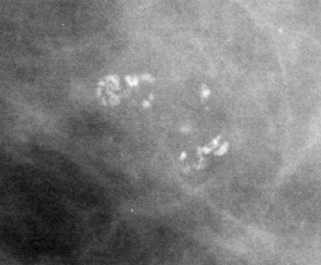
Cropped region of a digitized screen-film mammogram centred on a radiologist-marked abnormality; left breast; CC view.
Calcifications, morphology pleomorphic, distribution clustered / segmental; BI-RADS assessment category 4; subtlety rating 4 on a 1 (subtle) to 5 (obvious) scale; pathology (as recorded): benign.